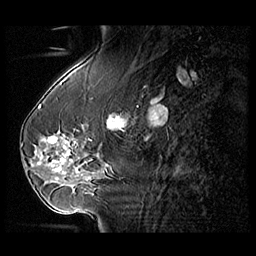
Breast MRI (dynamic contrast-enhanced), one sagittal slice. Slice 41 of 104 in the series (ordered by position). 3 images stored at this slice position (order not interpretable as contrast timing). 1.5 T. TE 1.3 ms, TR 5.5 ms. 3 mm slice thickness. 256 × 256 image matrix. Female patient, age 54 years. Case-level facts recorded for this patient, not image findings: setting: breast cancer imaged before/during neoadjuvant chemotherapy; receptor status: HR-positive, HER2-negative.
Outlined on this slice (semi-automatic segmentation, software-assisted and operator-edited):
- analysis volume of interest (the breast-tissue region the enhancement analysis was run in; not a lesion): bounding box [x1, y1, x2, y2] px = [28, 127, 104, 182]
- tumour enhancement mask (voxels above the 140 % enhancement threshold inside the analysis volume of interest): [39, 136, 69, 173]